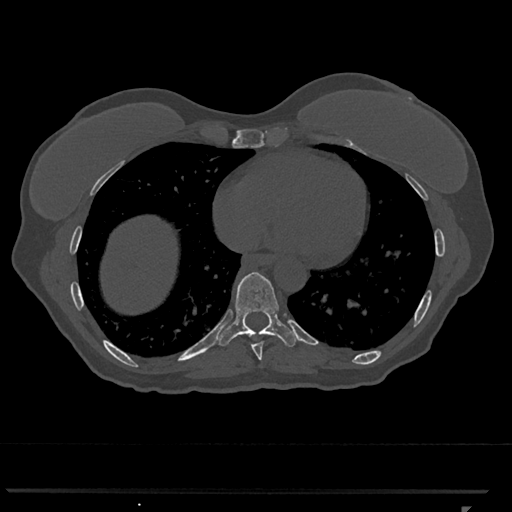
CT including the spine, one axial slice; slice 631 of 793 in the series (ordered by position); 120 kVp; bone window (W 1800 / L 400 HU); 512 × 512 image matrix, field of view 380 × 380 mm. Patient: female, 62 years. Case-level facts recorded for this patient, not image findings: primary cancer: renal.
Annotated regions visible in this slice (semi-automatic segmentation, software-assisted and operator-edited):
- T8 vertebra: box from (x=251, y=342) to (x=263, y=360) px
- T9 vertebra: (x=217, y=272)–(x=298, y=347)